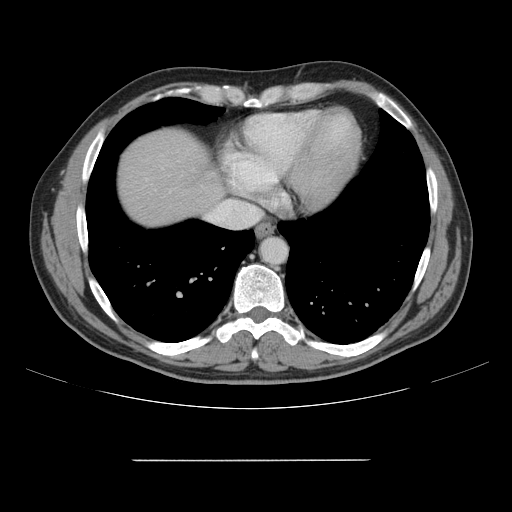
Contrast-enhanced abdominal CT, one axial slice; position 144 of 164 along the scan axis; 120 kVp; intravenous contrast given; soft-tissue window (W 400 / L 40 HU); 512 × 512 image matrix, field of view 404 × 404 mm. Male patient, age 54 years. Case-level facts recorded for this patient, not image findings: diagnosis: colorectal cancer liver metastases, imaged before liver resection; multiple liver metastases: yes; largest metastasis: 1 cm; disease in both lobes: no.
Structures marked on this image (outlined manually by an expert reader):
- hepatic veins: bounding box (x1, y1, x2, y2) in pixels: (207, 200, 258, 225)
- liver: (118, 129, 221, 226)
- planned liver remnant (the part of the liver to remain after resection): (118, 129, 223, 226)